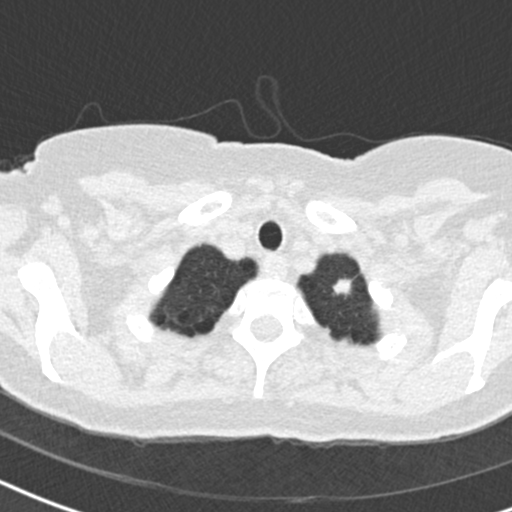
Low-dose screening chest CT, one axial slice. Slice 172 of 184 in the series (ordered by position). Lung window (W 1500 / L -600 HU). 2 mm slice thickness. 512 × 512 image matrix.
Annotated regions visible in this slice (expert manual segmentation):
- lesion 1 (tumor, upper lobe of left lung): bounding box [x1, y1, x2, y2] px = [333, 279, 352, 295]